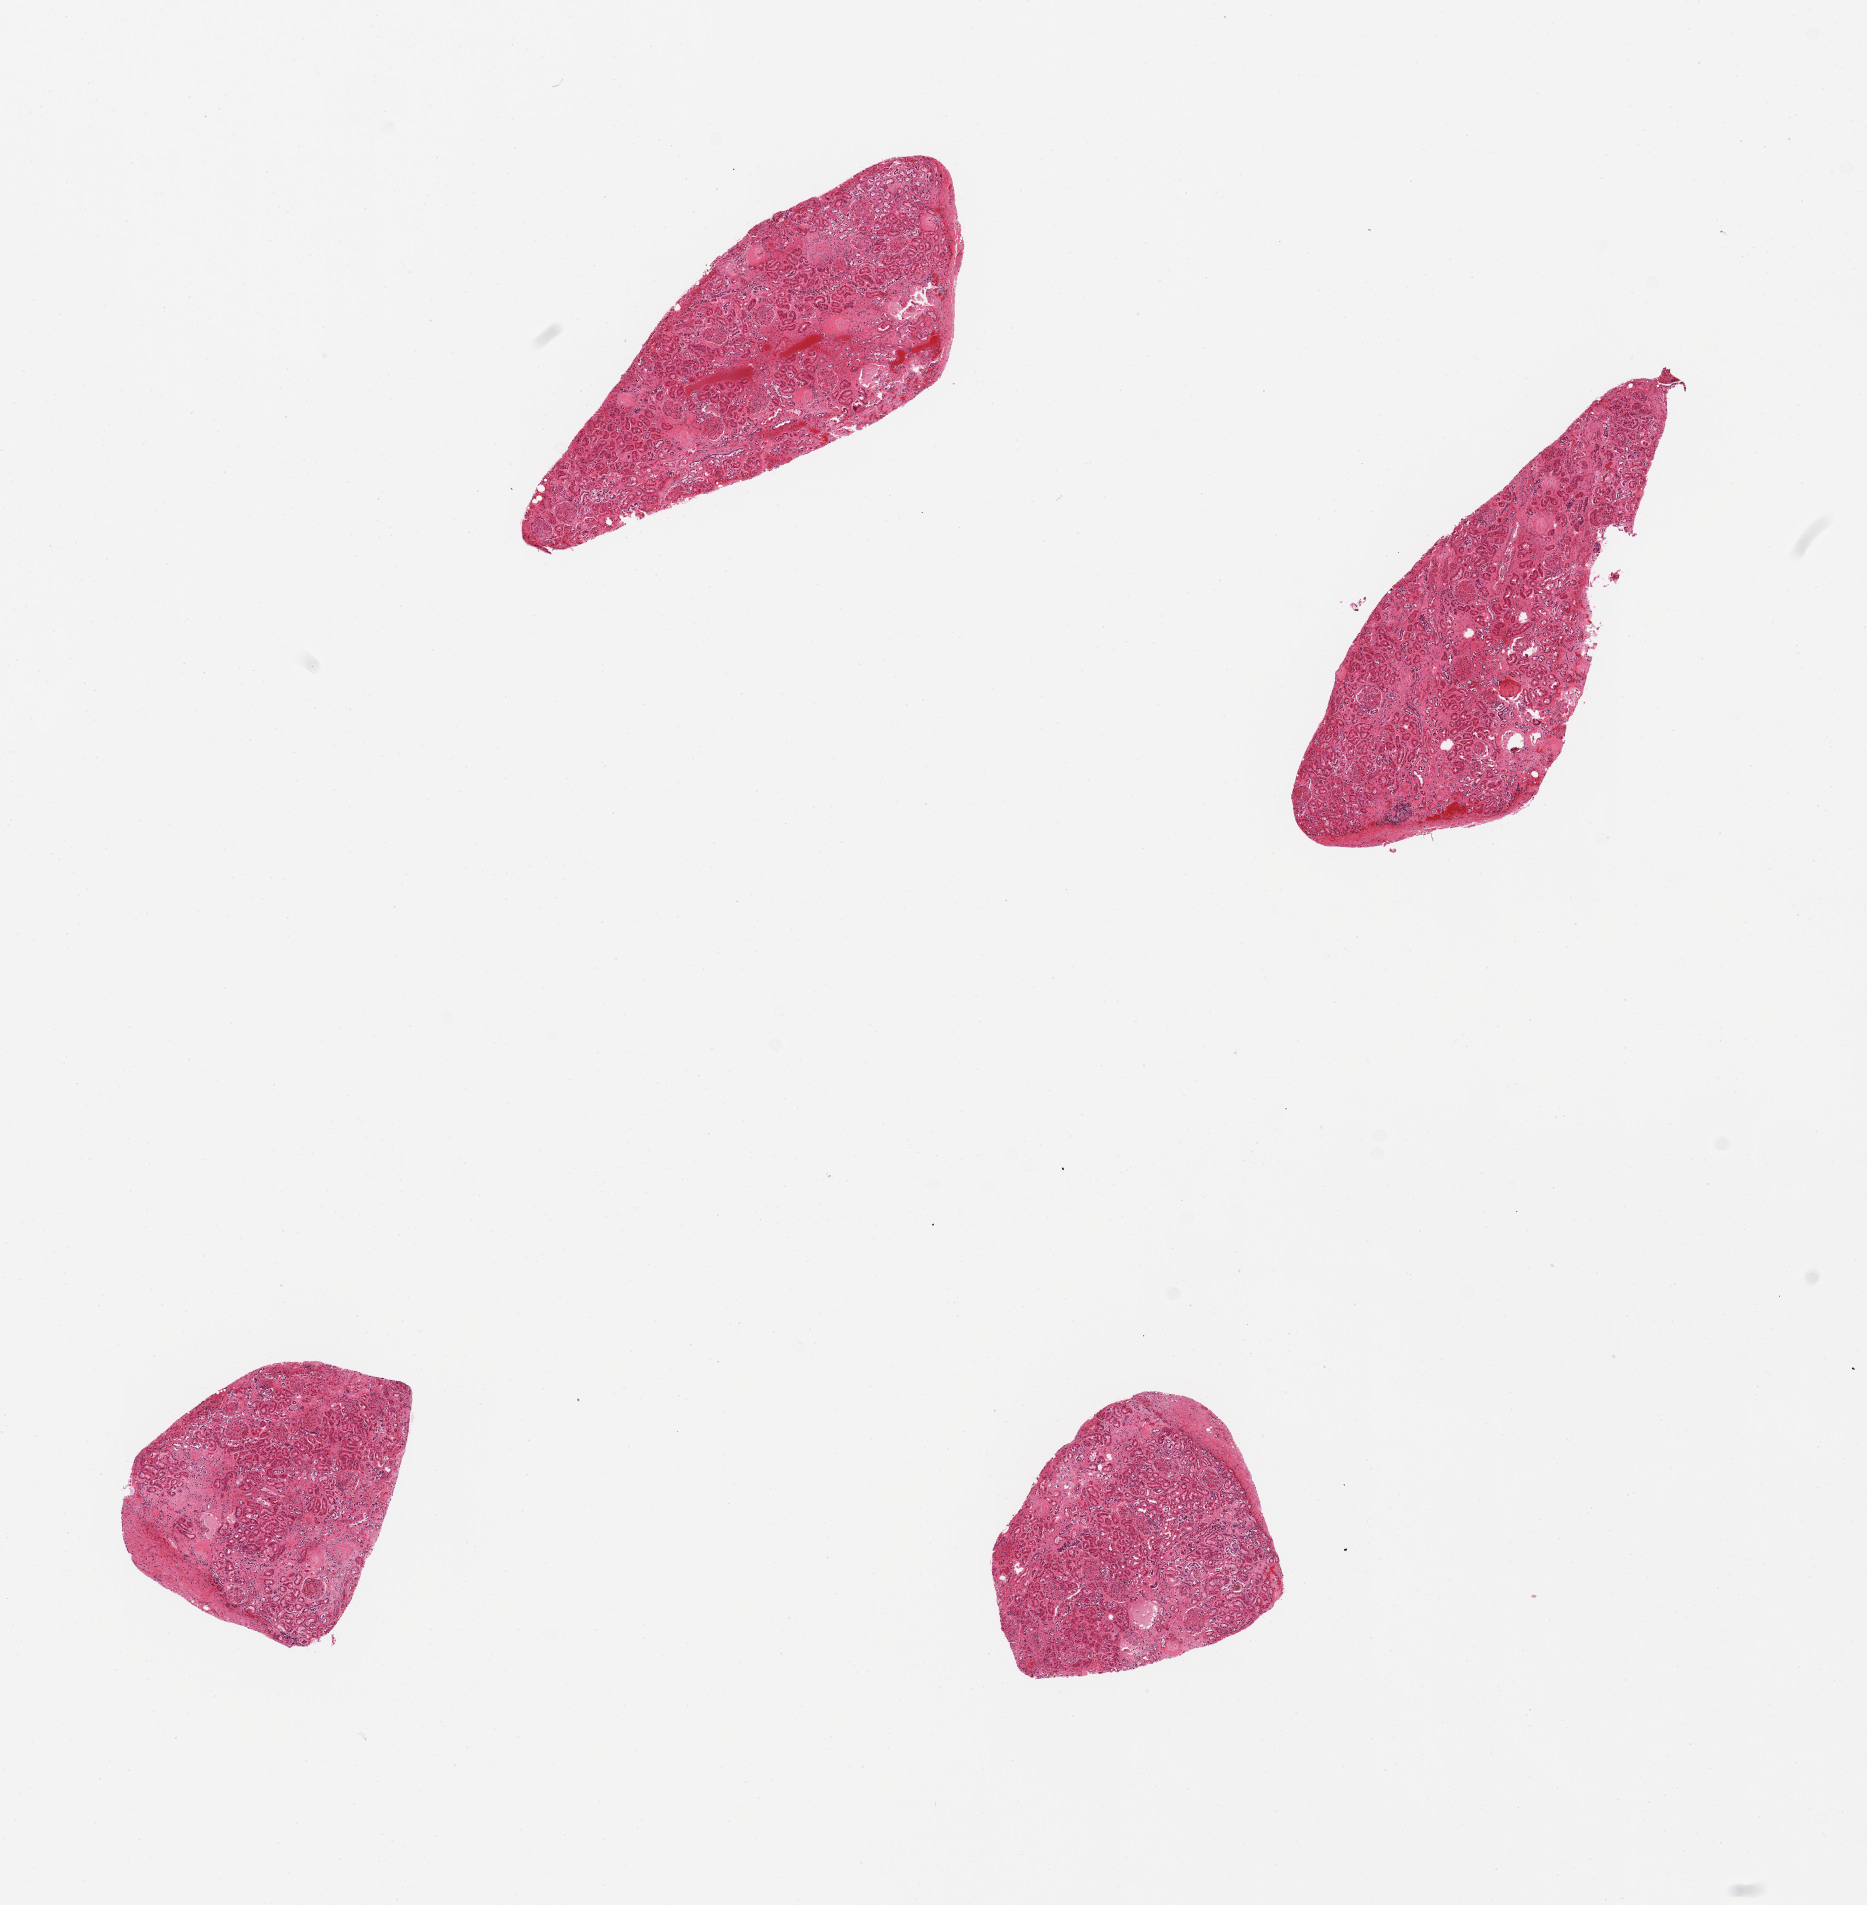
Whole-slide image, H&E stain — shown as a low-resolution overview of the whole scanned area (about 14.8 x 15.1 mm); PAXgene-fixed, paraffin-embedded tissue; target tissue: renal cortex; donor tissue sample. Male donor.
Review note (as recorded): 4 pieces, glomeruli in all sections, glomerulosclerosis.